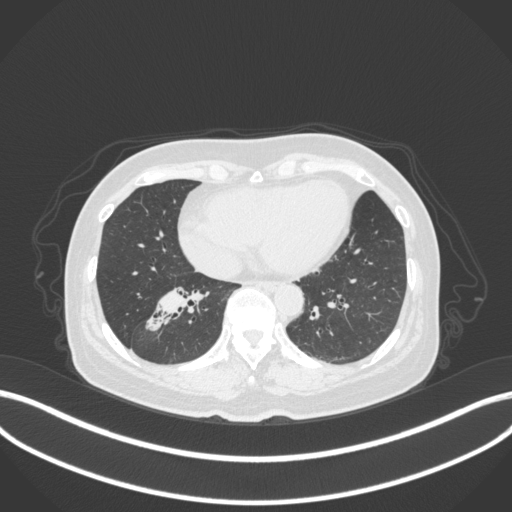
Chest CT, one axial slice; position 136 of 429 along the scan axis; reconstruction kernel B31f; 120 kVp; lung window (W 1500 / L -600 HU); 1 mm slice thickness; 512 × 512 image matrix. Female patient, age 67 years. Case-level facts recorded for this patient, not image findings: clinical TNM (as recorded): T1c N1 M0; histopathological grade: G2-3.
Structures marked on this image (rectangle marked by the reading radiologist):
- lung tumour (recorded histology: adenocarcinoma): bounding box [x1, y1, x2, y2] px = [140, 283, 218, 340]